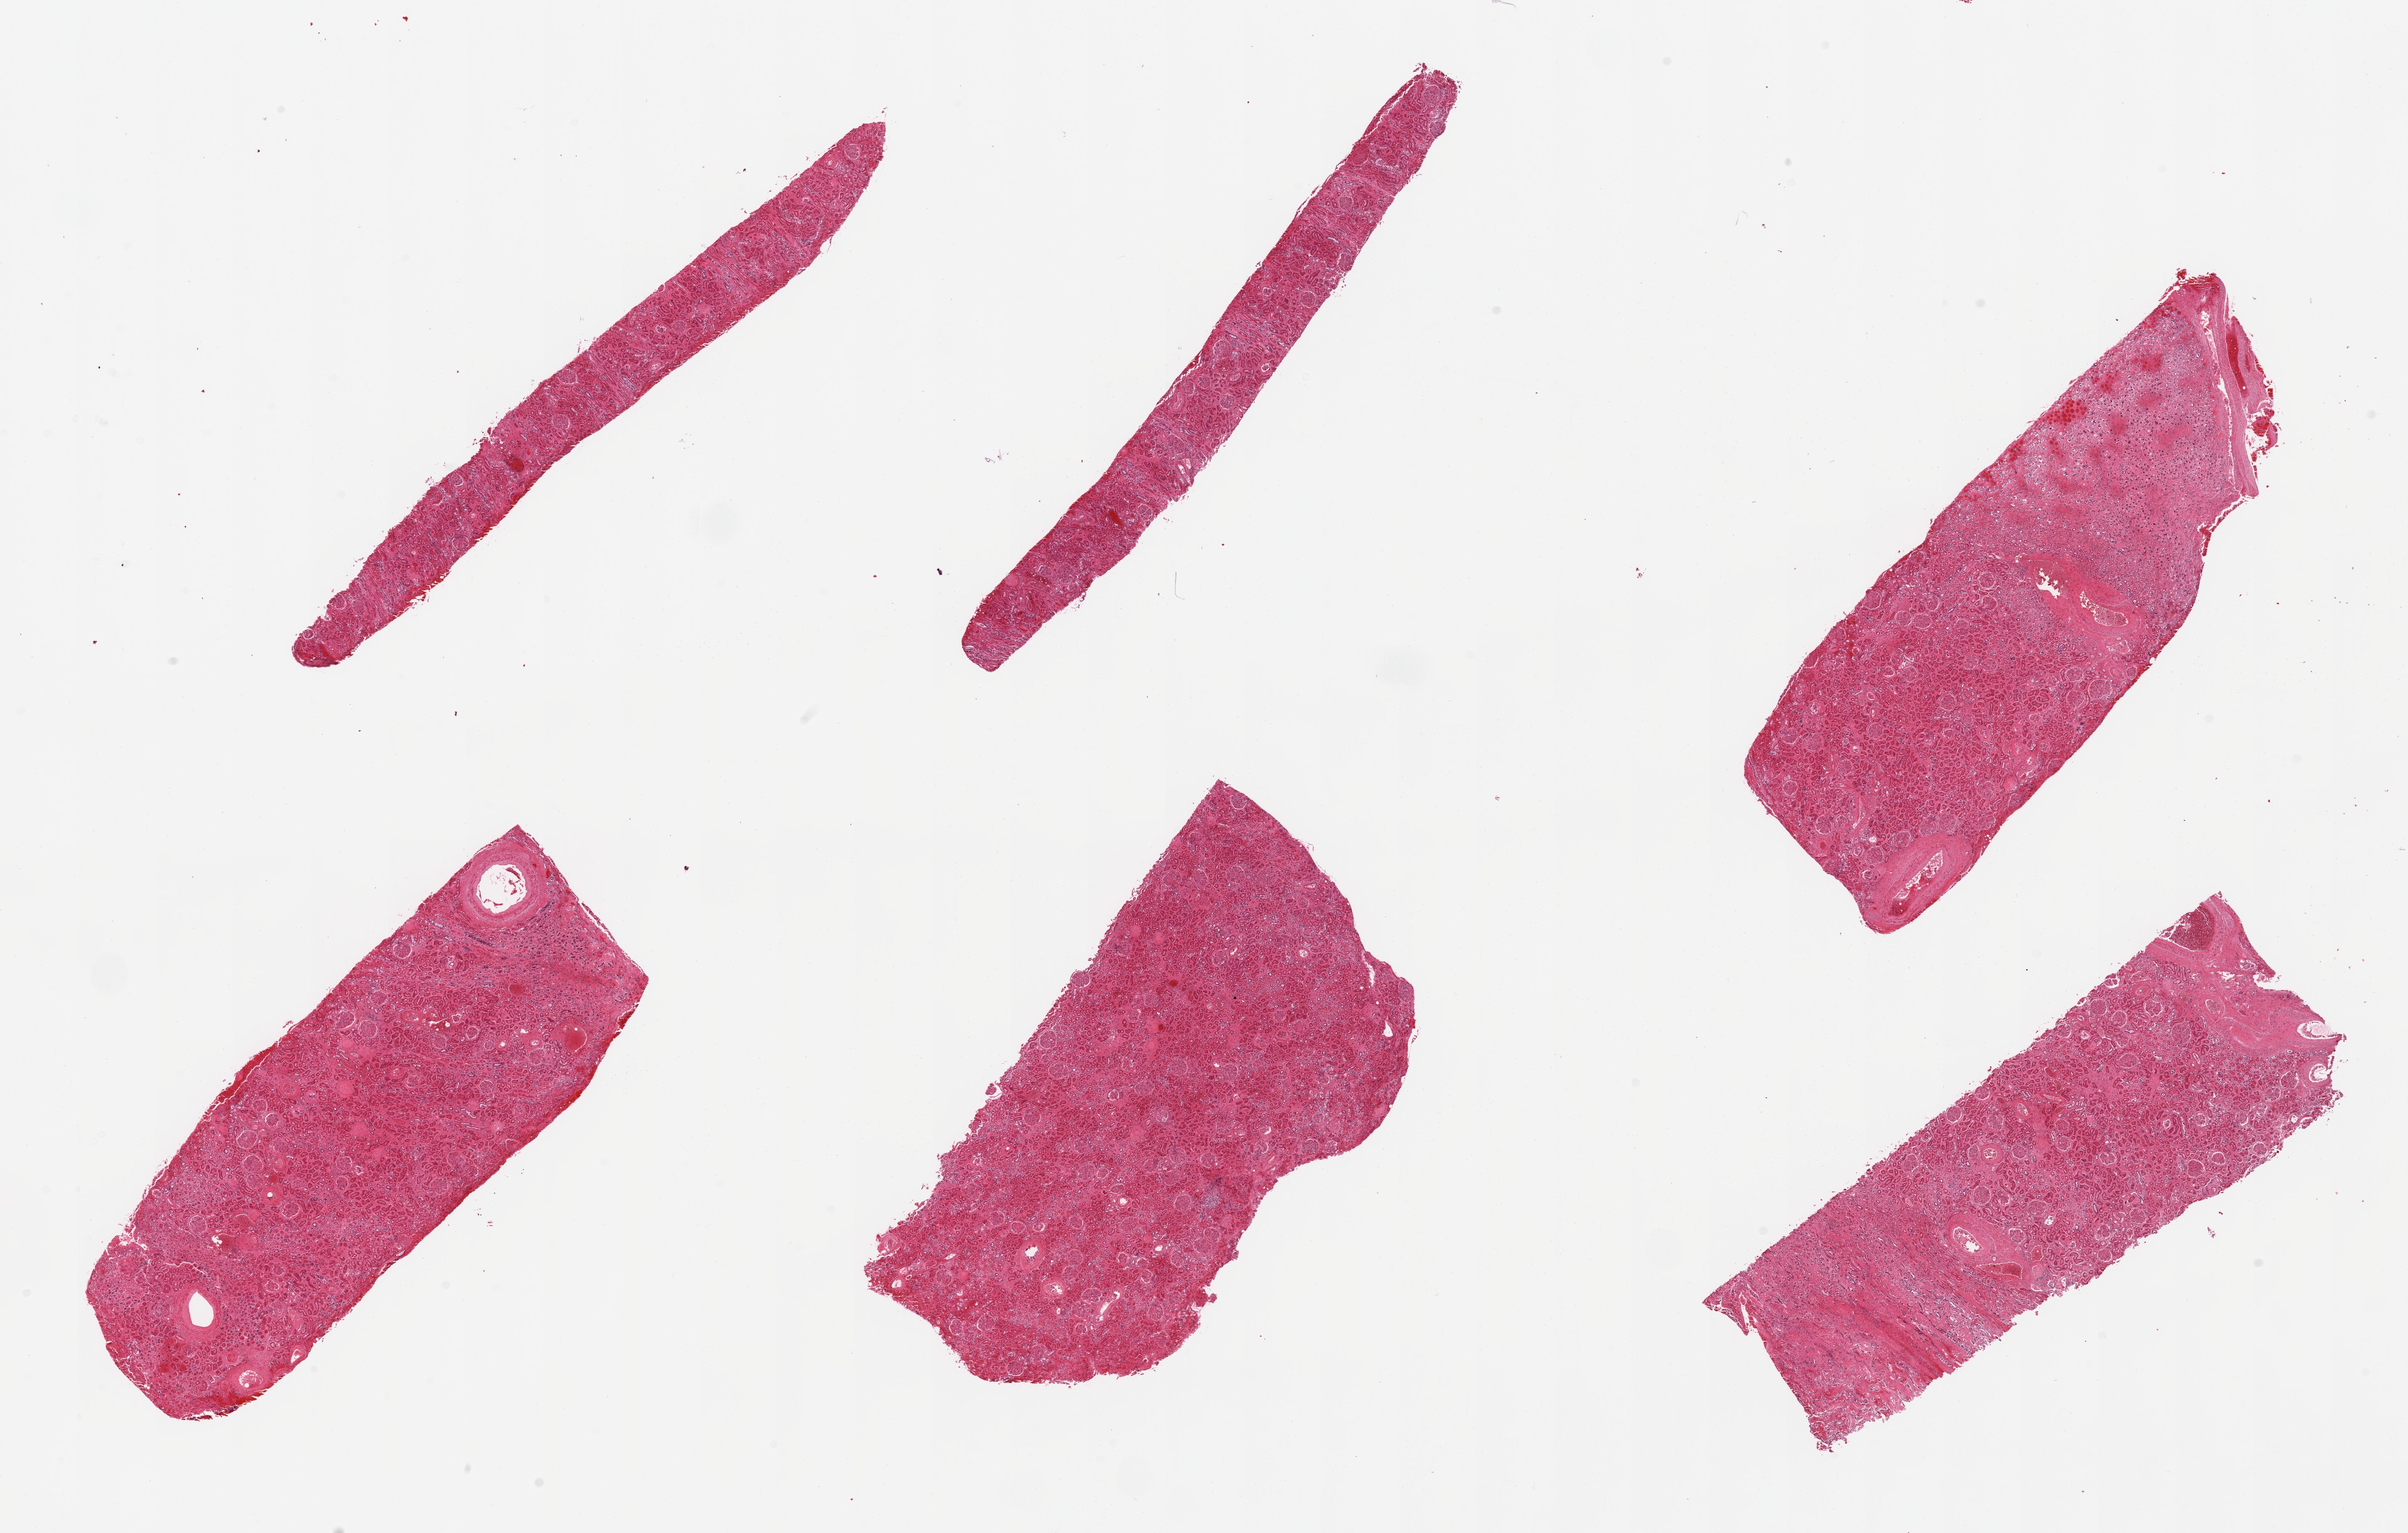
Hematoxylin and eosin (H&E) whole-slide image — a low-resolution overview of the entire scanned area, about 30.5 x 19.4 mm. PAXgene-fixed paraffin-embedded (PFPE) section. Target tissue: renal cortex. Tissue donor sample. Donor: male.
Pathologist's review note for this sample: 6 pieces; scattered 'diabetic' glomerulosclerosis; admixture with medulla.